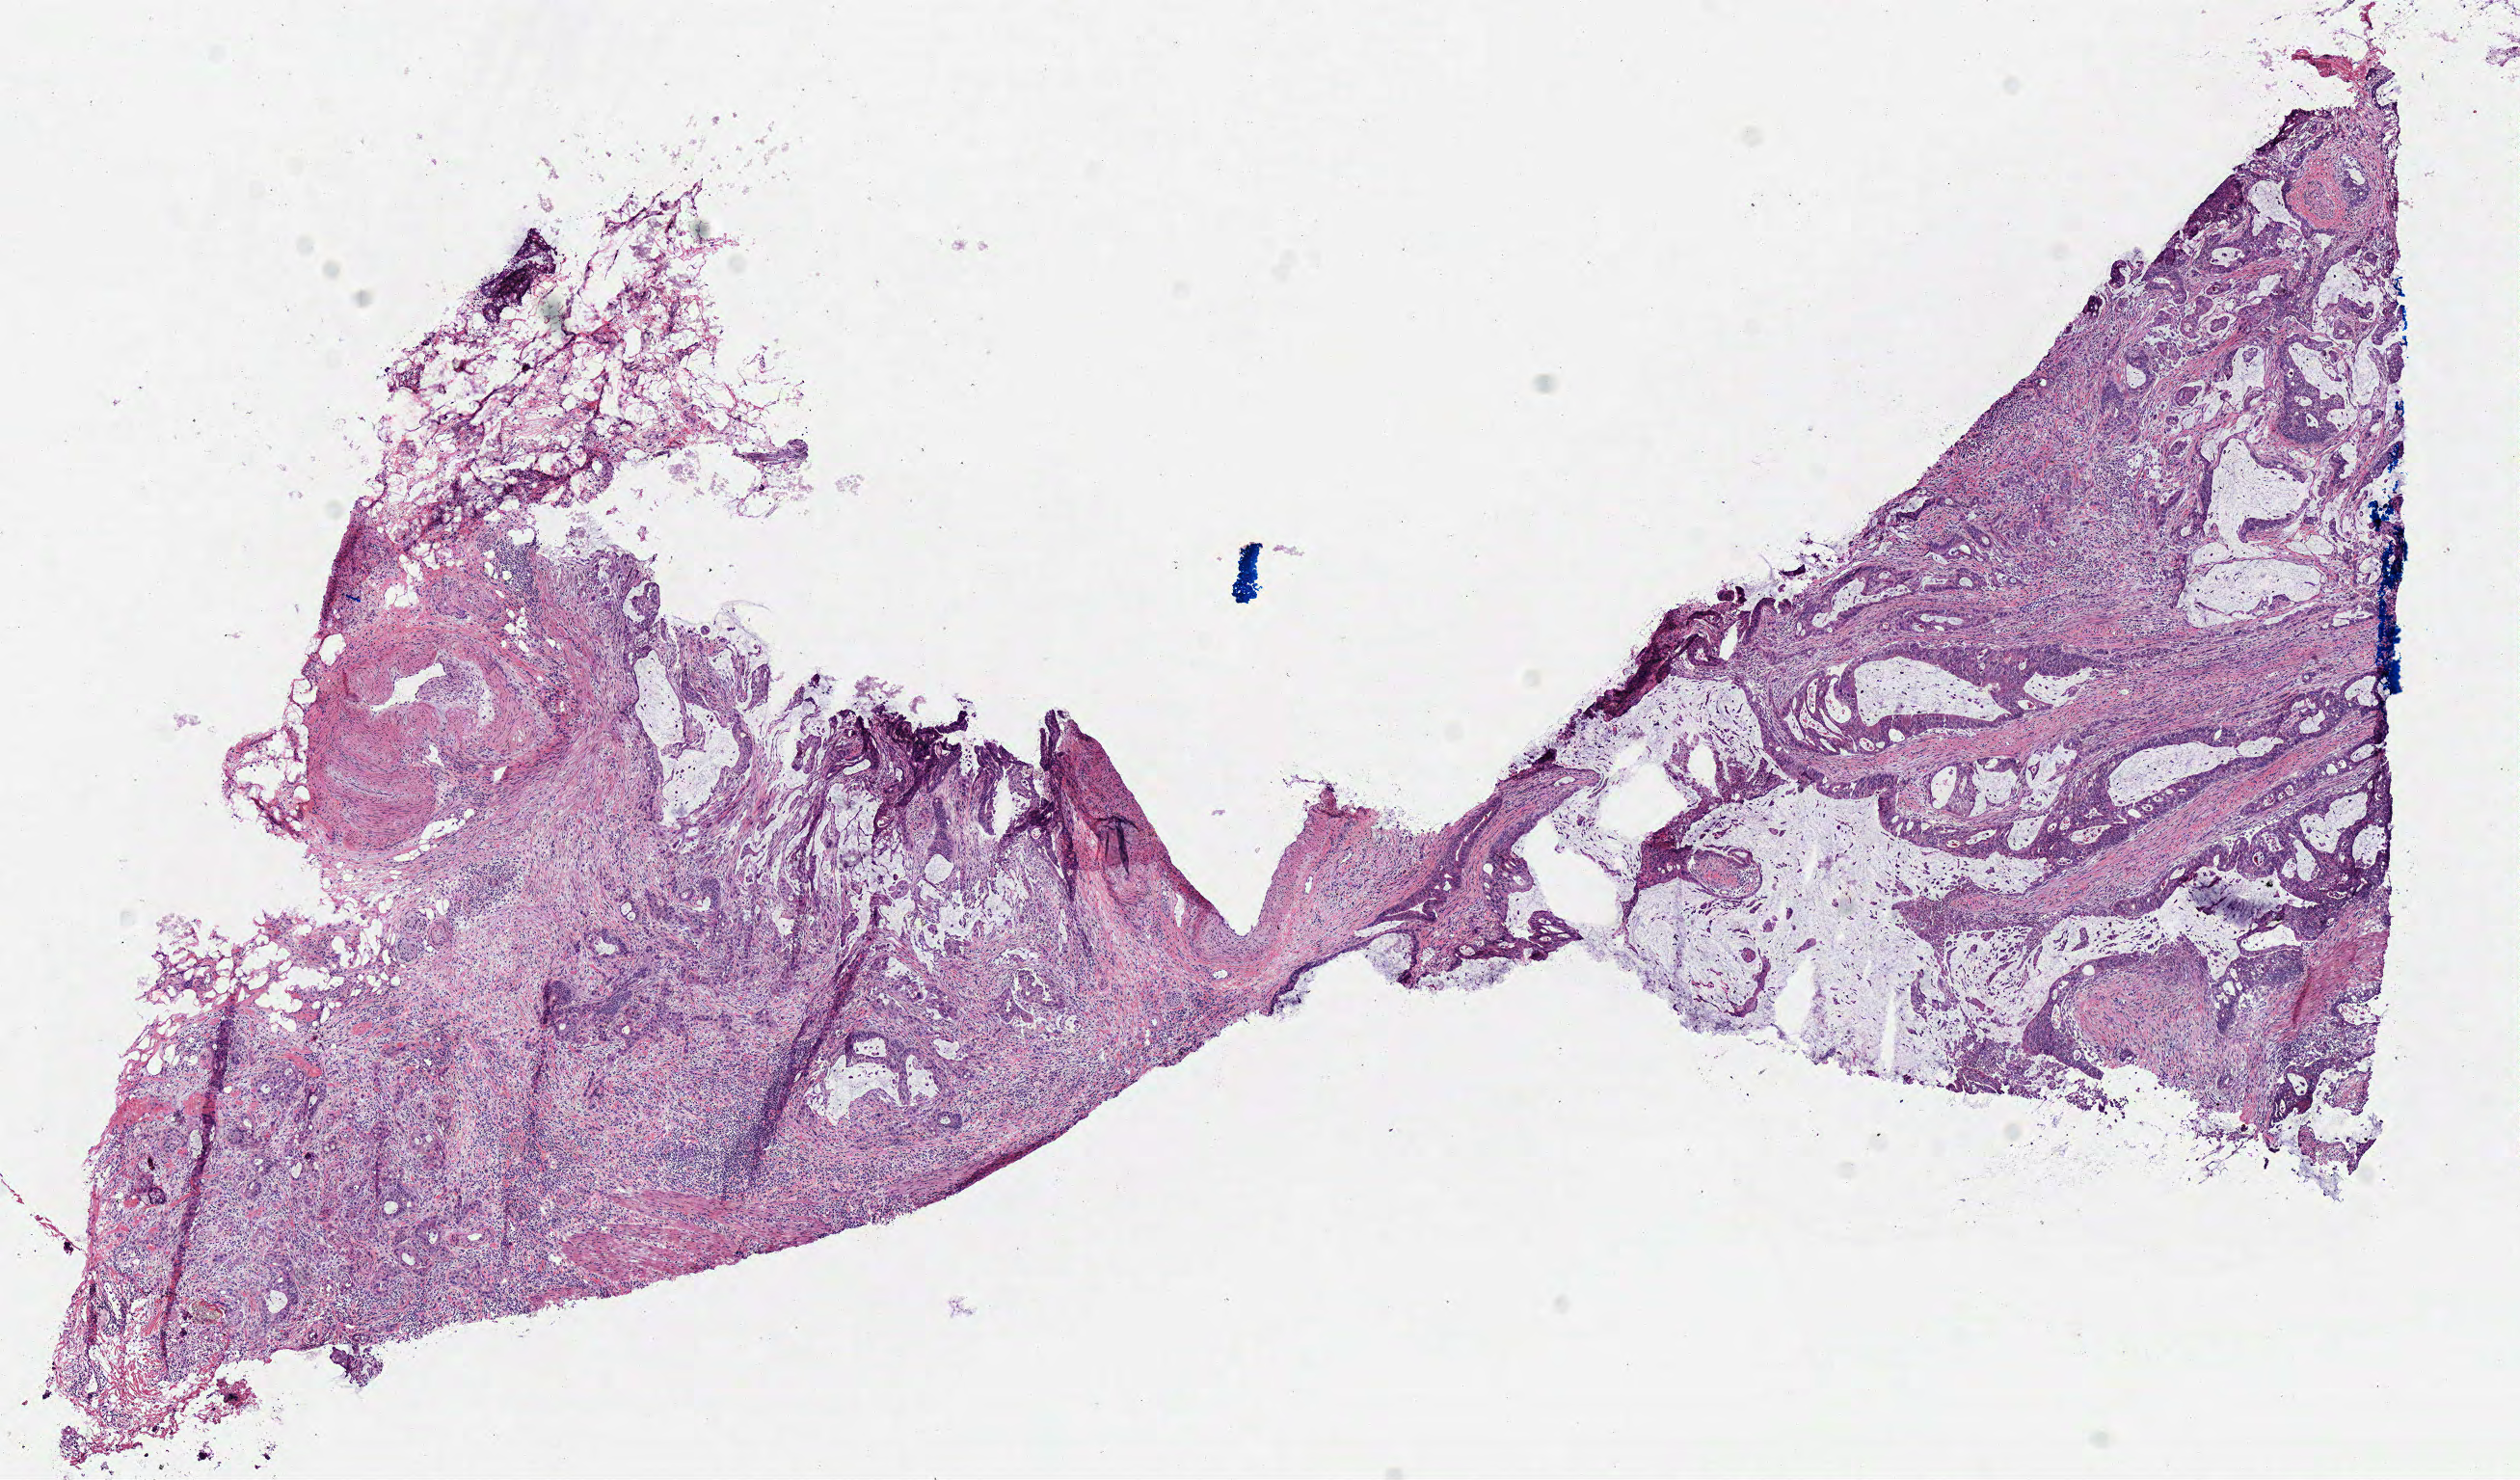
Digitized H&E tissue section (whole slide), low-resolution overview of the scanned area, about 10.3 x 6.0 mm (slide scanned at 40x), frozen section, primary tumour sample from the colon. Patient: female, age at initial diagnosis 62 years. Slide review estimates, as recorded: tumour cells 80%, tumour nuclei 80%, normal cells 20%, stromal cells 0%, necrosis 0%. Inflammatory infiltration, as recorded: lymphocyte infiltration 5%, monocyte infiltration 1%, neutrophil infiltration 2%.
Diagnosis: Mucinous adenocarcinoma. Lymph nodes positive (case pathology): 0 of 22 examined. AJCC pathologic stage: IIA (7th edition).